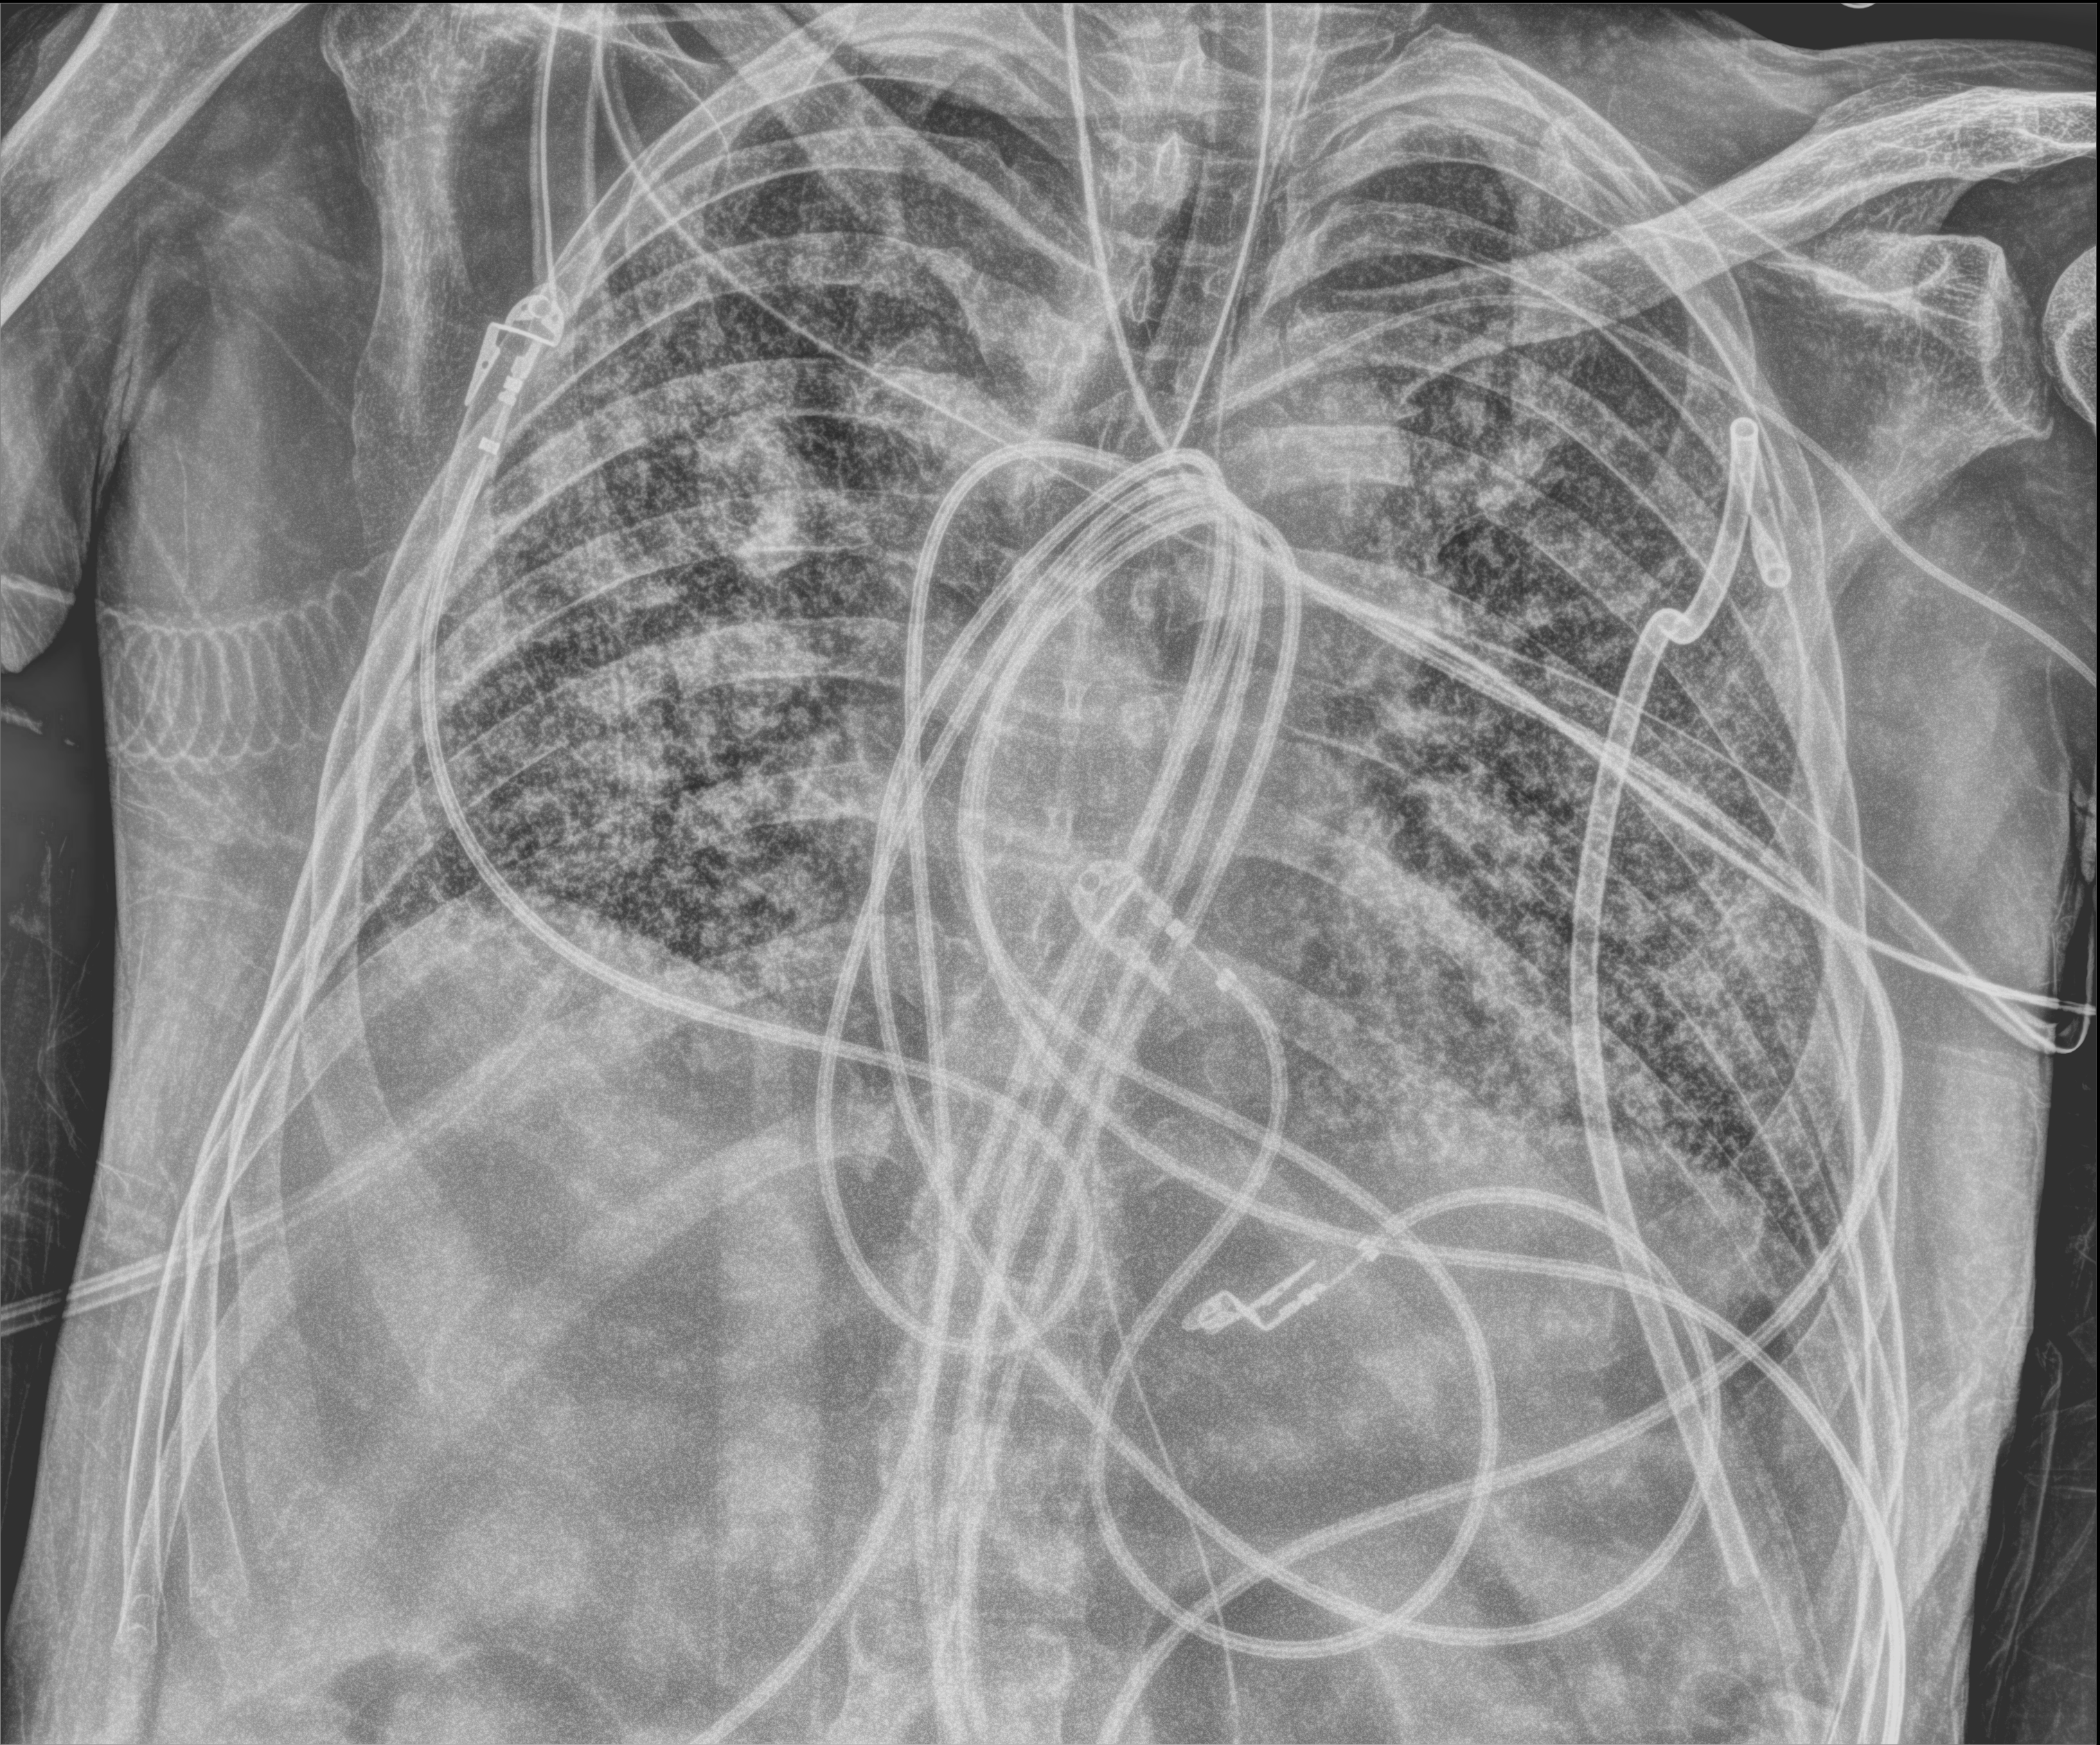
Portable chest radiograph; anteroposterior (AP) projection. Patient hospitalised with COVID-19; male, aged 60–74 years.
From the hospital-stay record, not from the radiograph (when in the stay this image was taken is not recorded): mechanically ventilated during this hospital stay: yes.